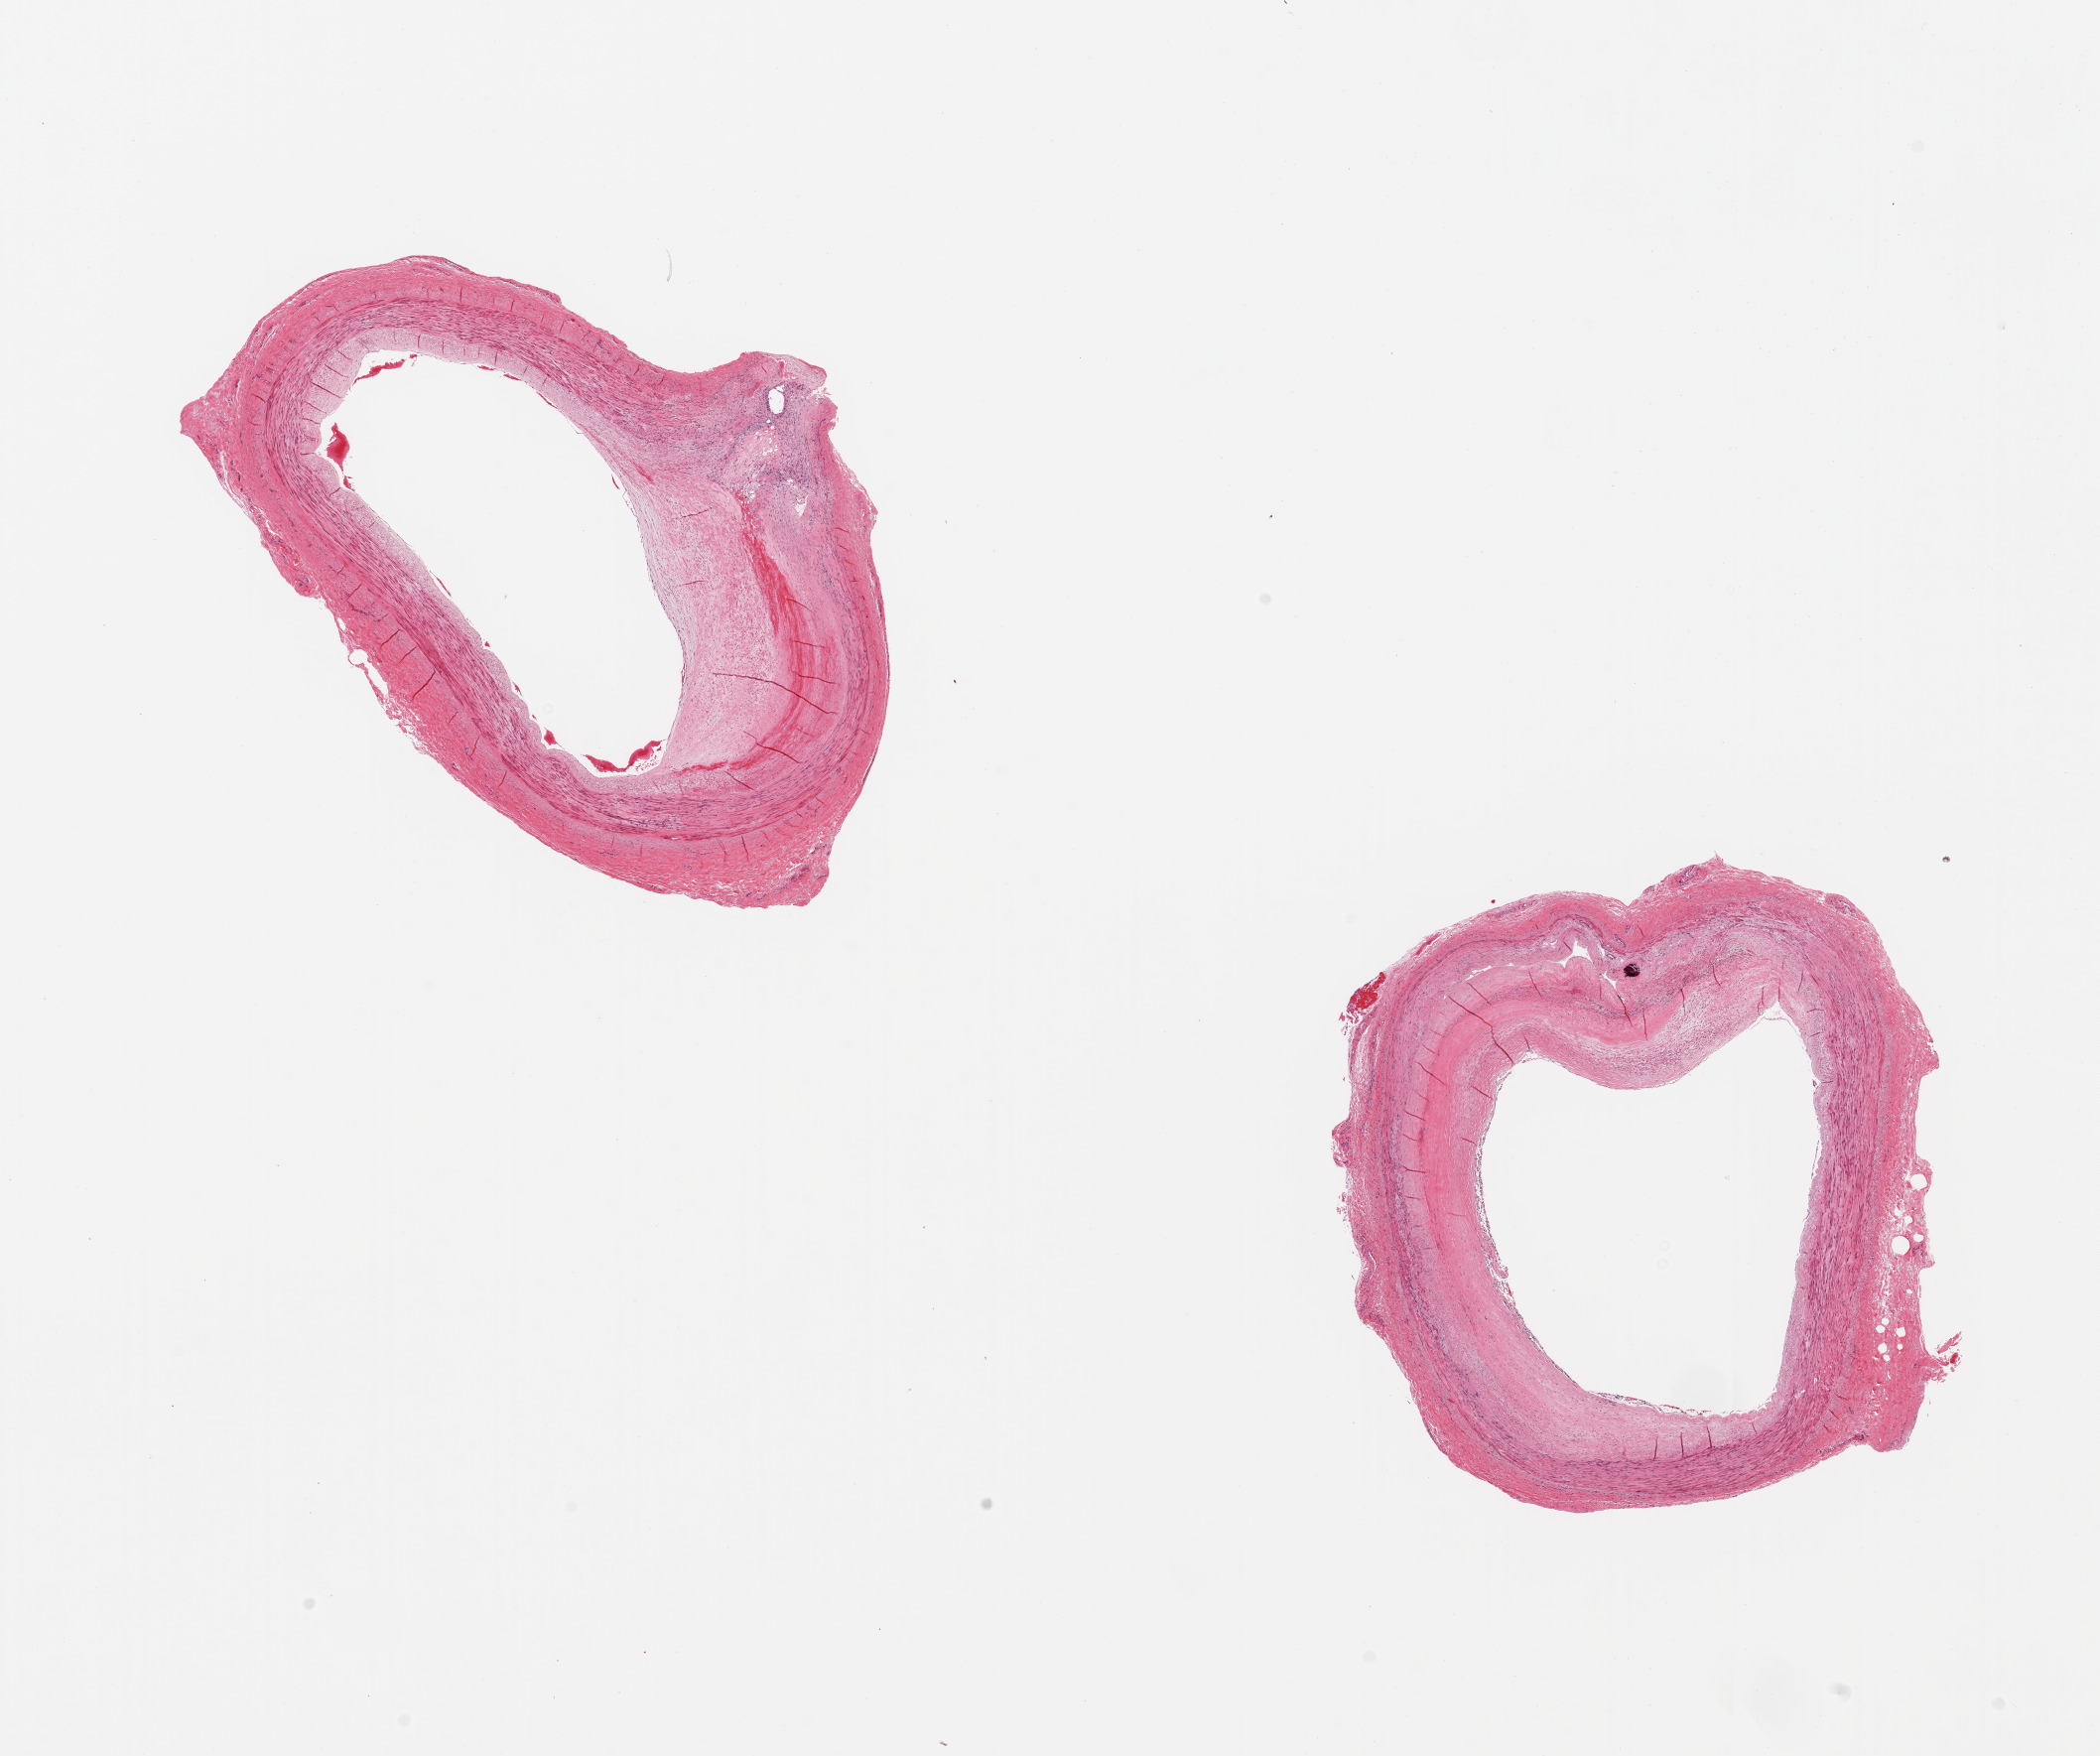
Digitized hematoxylin and eosin (H&E)-stained section — whole scanned area (about 16.7 x 14.0 mm, slide scanned at 20x) shown as a low-resolution overview; PAXgene-fixed paraffin-embedded (PFPE) section; sampled site (target tissue): tibial artery; tissue donor sample.
Pathologist's review note for this sample: 2 pieces, ~20-30% luminal atherotic occlusion; no adherent fat.